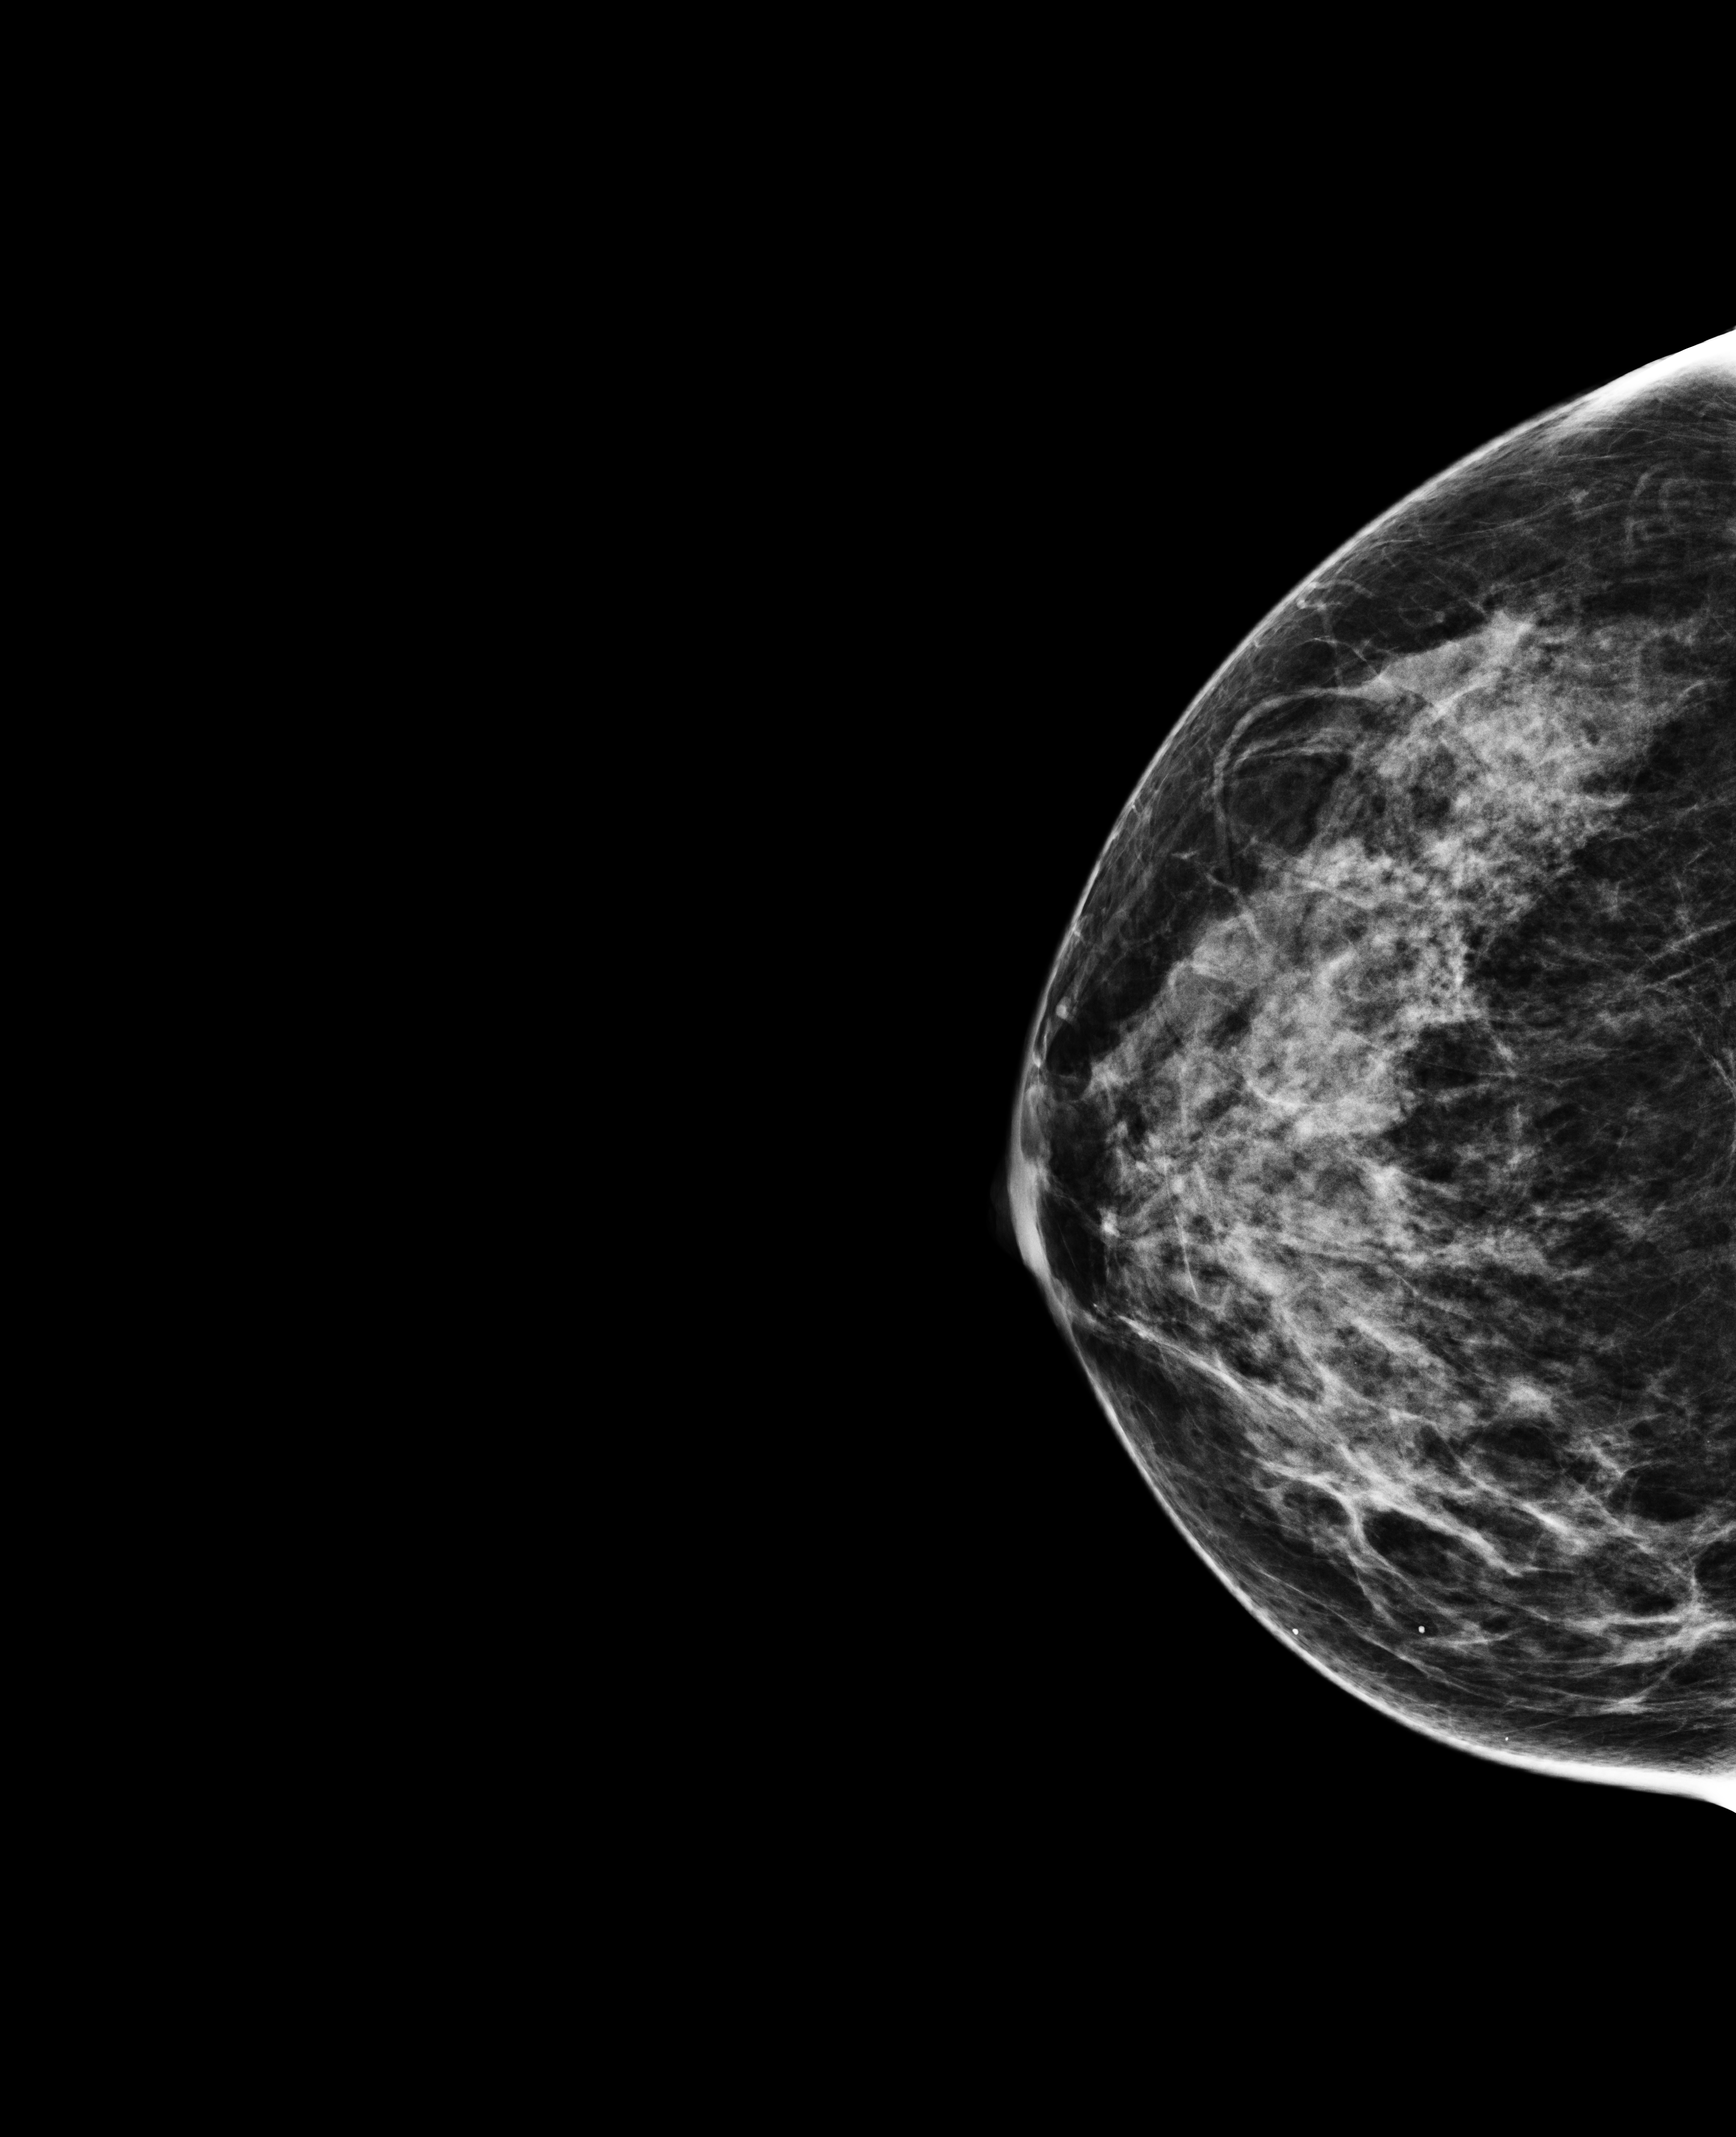
Annual screening mammography examination. Female patient, age 47 years.
Image type: full-field digital mammogram. Breast: right. Projection: cranio-caudal projection.